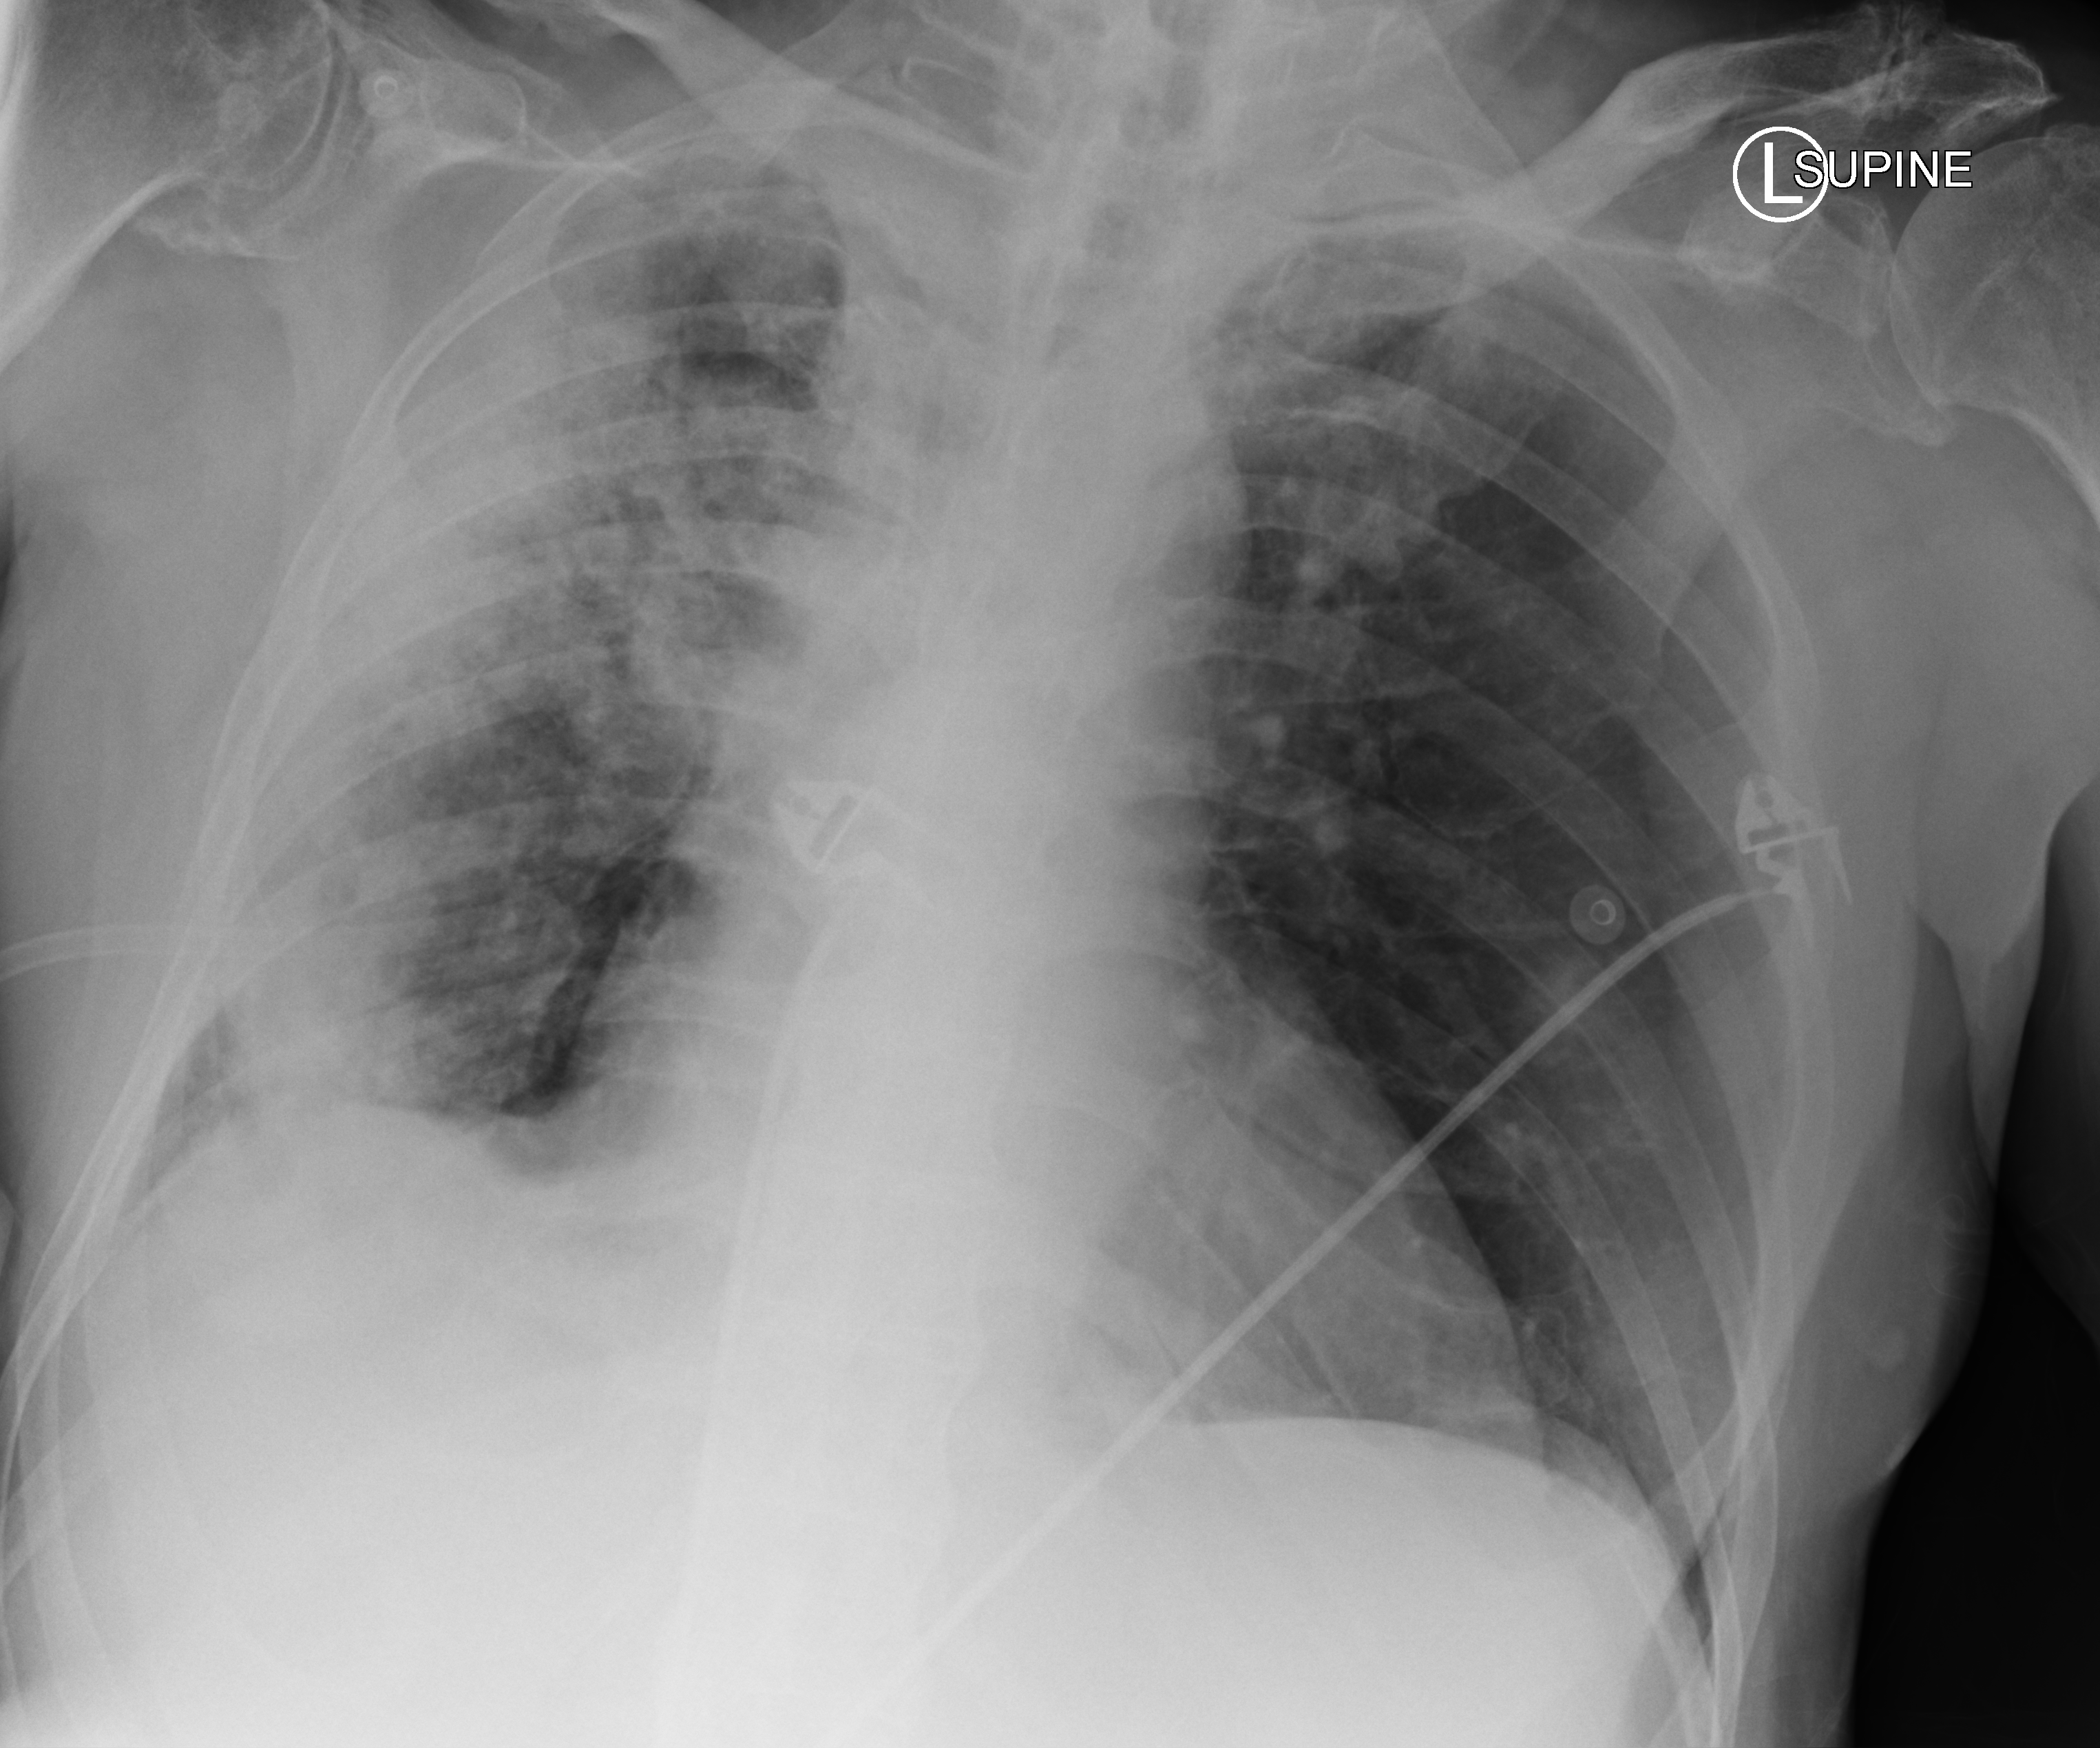
Portable chest radiograph, anteroposterior (AP) projection. Male patient hospitalised with COVID-19, age 75–90 years.
From the hospital-stay record, not from the radiograph (when in the stay this image was taken is not recorded): admitted to intensive care during this hospital stay: no; mechanically ventilated during this hospital stay: no; length of hospital stay: 15 days.